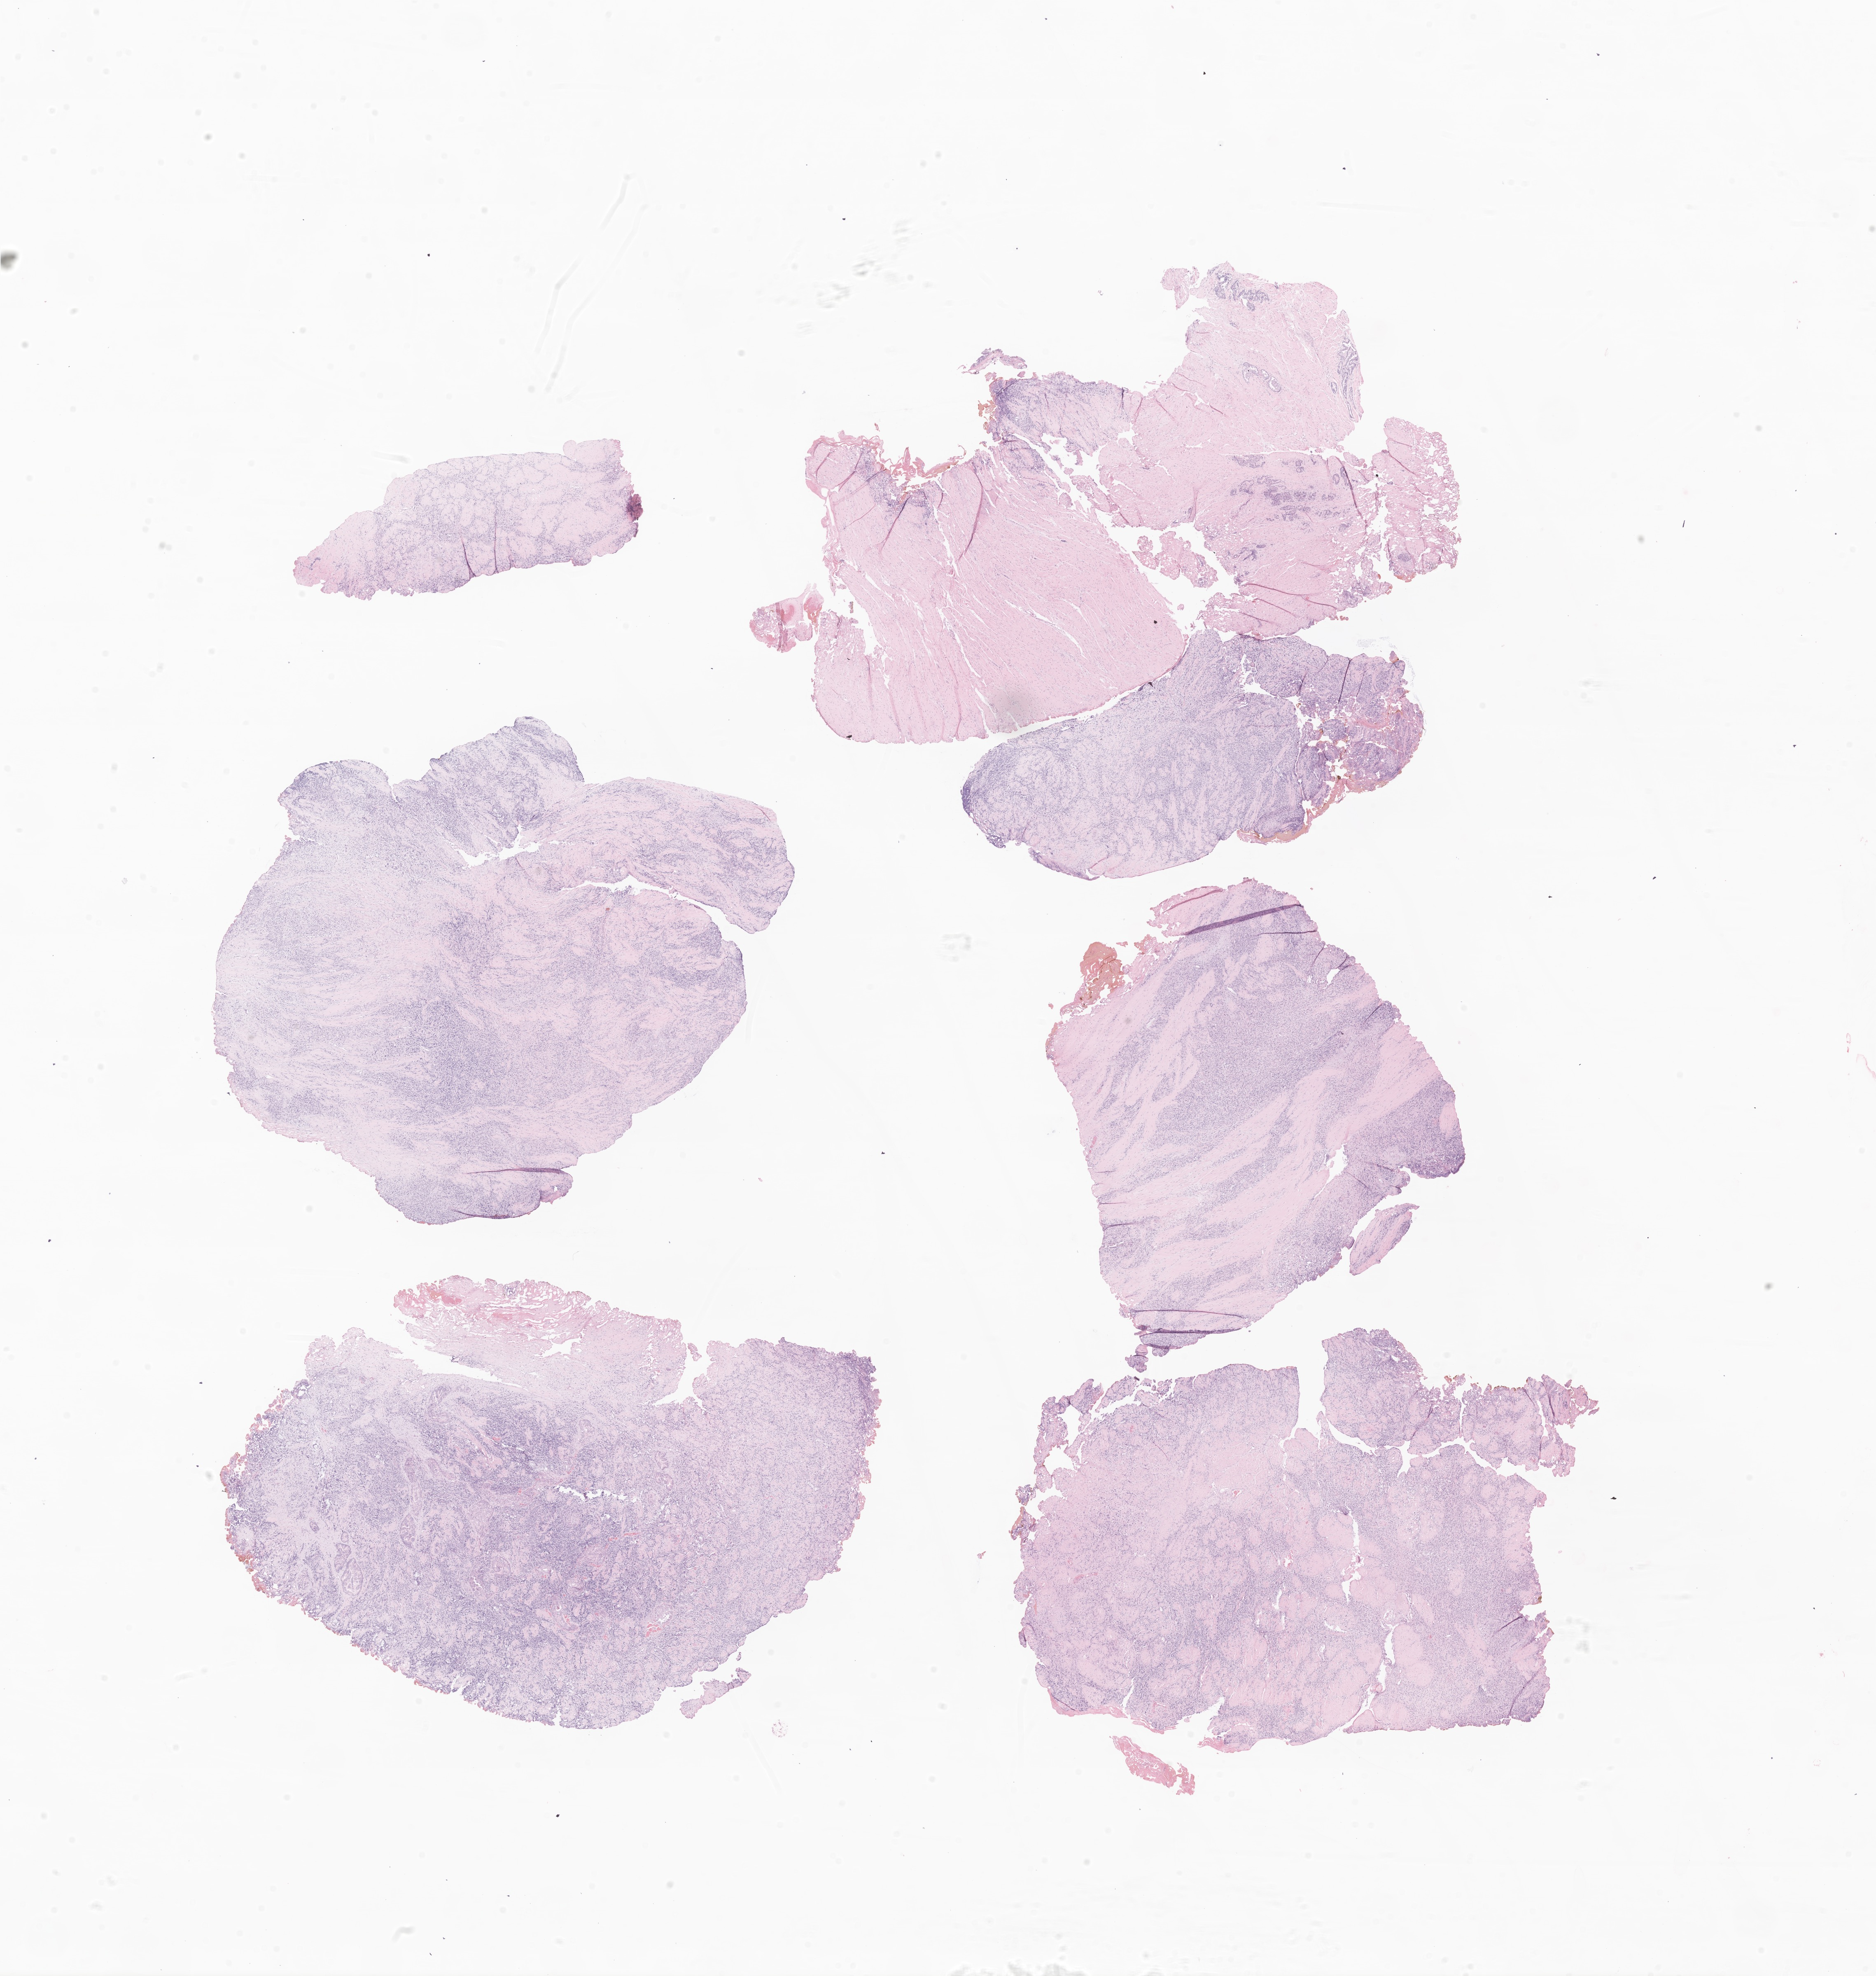
Digitized hematoxylin and eosin (H&E)-stained section of tumor tissue from the urinary system, a low-resolution overview of the entire scanned area, about 19.2 x 20.2 mm. Formalin-fixed, paraffin-embedded (FFPE) tissue. Male patient, age 177 months (14 years 9 months).
• diagnosis (ICD-O-3 morphology term): Rhabdomyosarcoma, NOS